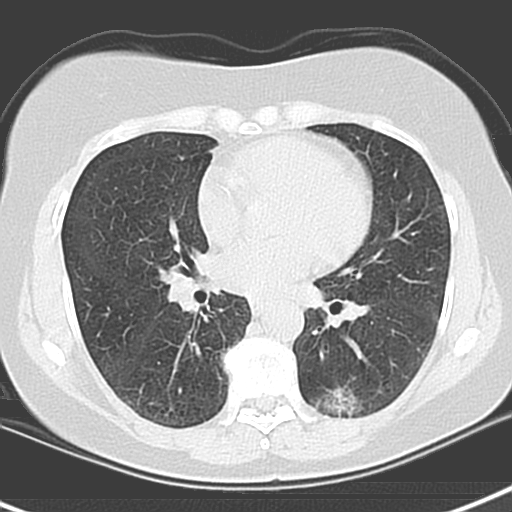
Axial slice from a low-dose chest CT screening exam, baseline annual screen, lung window (W 1500 / L -600 HU), 3.2 mm slice thickness, standard (soft-tissue) reconstruction kernel (B), slice 74 of 129 in the series, 512 × 512 image matrix. Female, age 55 years at enrolment. Current smoker at enrolment.
• Lesion marked by an expert reader, box from (x=312, y=374) to (x=388, y=423) px.
• The screening reader recorded 3 non-calcified nodules or masses ≥4 mm on this exam; which of them this box marks is not recorded.
• Official screen result: positive, change unspecified: nodule(s) >= 4 mm or enlarging nodule(s), mass(es), or other non-specific abnormalities suspicious for lung cancer.
• Lung cancer was diagnosed 1063 days after this screen (after the third annual screen): adenocarcinoma with mixed subtypes, left lower lobe, poorly differentiated (G3), stage IA (AJCC 6th edition), 21 mm at pathology.